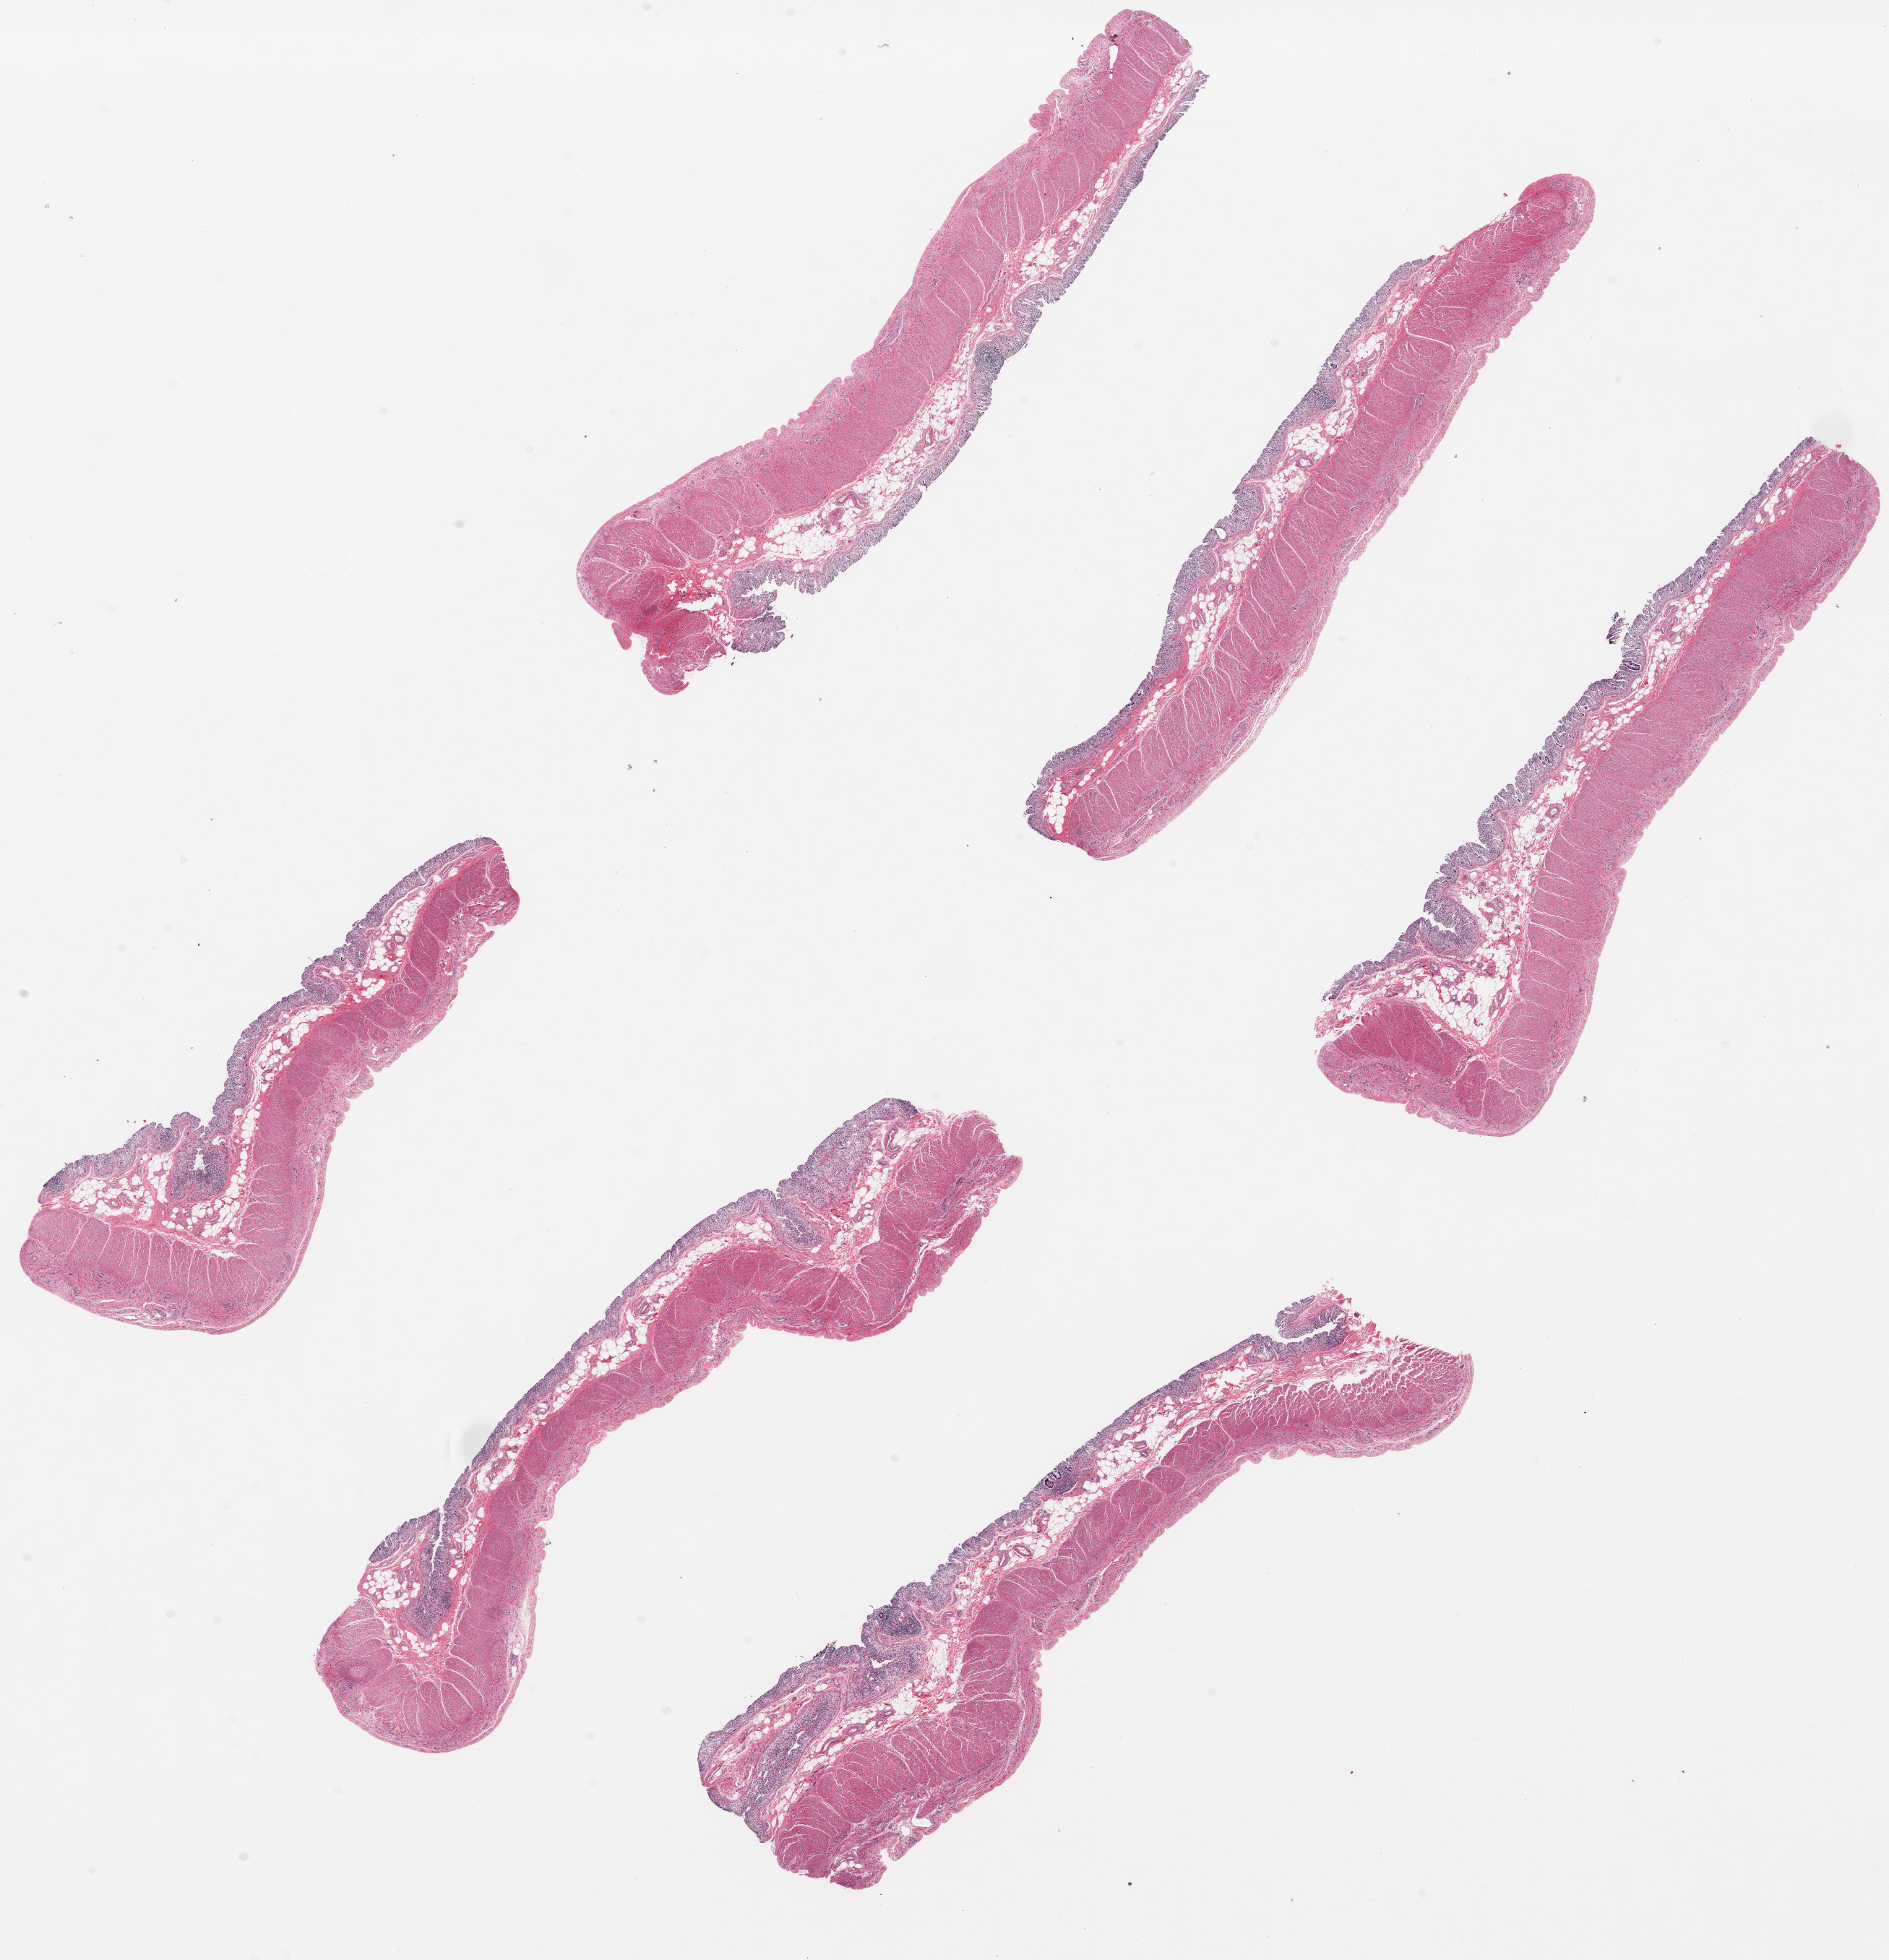
Whole-slide image, haematoxylin and eosin stain, whole scanned area (about 20.7 x 21.4 mm, slide scanned at 20x) shown as a low-resolution overview, PAXgene-fixed, paraffin-embedded tissue, section of transverse colon (target tissue), donor tissue sample.
Reviewer comment on this tissue sample: 6 ~9x1.5mm pieces. Epithelium totally autolyzed; mucosal stroma is ~10-12% of thickness.